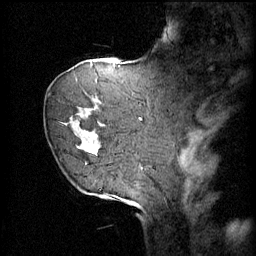
Breast MRI (dynamic contrast-enhanced), one sagittal slice; position 15 of 60 along the scan axis; 4 images stored at this slice position (order not interpretable as contrast timing); 1.5 T; TE 4.2 ms, TR 11 ms; 2 mm slice thickness; 256 × 256 image matrix, field of view 220 × 220 mm. Female patient, age 72 years.
Structures marked on this image (semi-automatically segmented with operator editing):
- analysis volume of interest (the breast-tissue region the enhancement analysis was run in; not a lesion): bounding box <59,68,109,163> (left, top, right, bottom; pixels)
- tumour enhancement mask (voxels above the 70 % enhancement threshold inside the analysis volume of interest): <68,72,108,151>